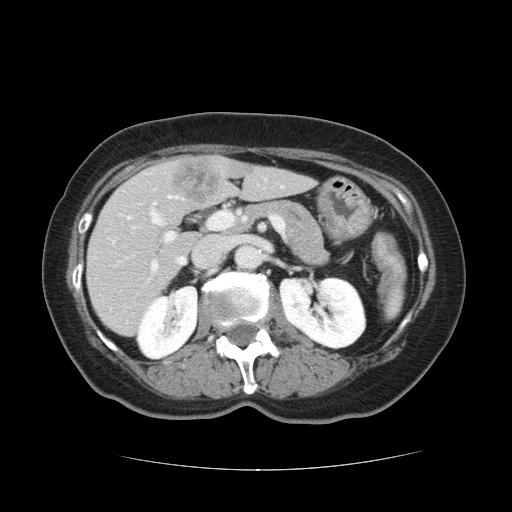
Contrast-enhanced abdominal CT, one axial slice. Position 61 of 128 along the scan axis. Intravenous contrast given. Soft-tissue window (W 400 / L 40 HU). 512 × 512 image matrix, field of view 366 × 366 mm. Female patient, age 67 years. From the clinical record (not read from this slice): diagnosis: colorectal cancer liver metastases, imaged before liver resection; multiple liver metastases: yes; largest metastasis: 3 cm; disease in both lobes: yes.
Structures marked on this image (expert manual segmentation):
- hepatic veins: box from (x=129, y=195) to (x=185, y=265) px
- liver: (x=87, y=156)–(x=313, y=336)
- planned liver remnant (the part of the liver to remain after resection): (x=87, y=165)–(x=313, y=336)
- portal vein (with intrahepatic branches): (x=112, y=202)–(x=232, y=273)
- liver metastasis: (x=167, y=162)–(x=220, y=203)